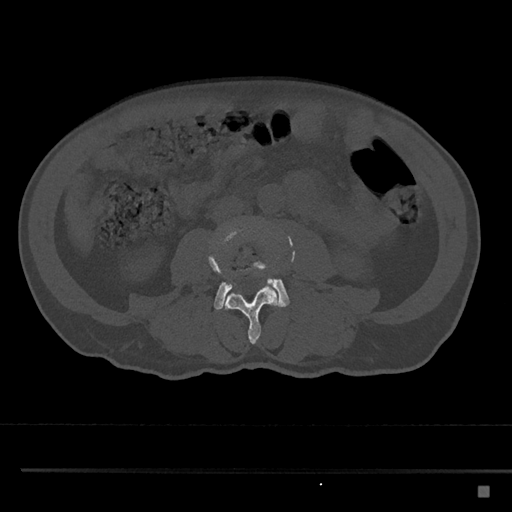
CT including the spine, one axial slice. Position 670 of 797 along the scan axis. Reconstruction kernel Br40s/3. Bone window (W 1800 / L 400 HU). 0.5 mm slice thickness. 512 × 512 image matrix, field of view 391 × 391 mm. Patient: male, 59 years. From the clinical record (not read from this slice): primary cancer: prostate.
Outlined on this slice (semi-automatic segmentation, software-assisted and operator-edited):
- L3 vertebra: box from (x=208, y=223) to (x=280, y=344) px
- L4 vertebra: (x=214, y=253)–(x=290, y=310)